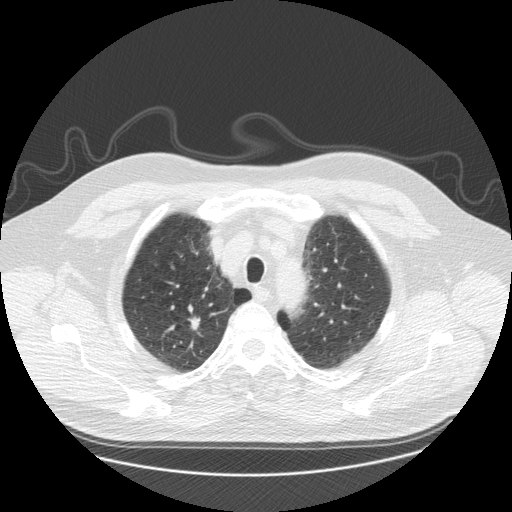
Axial slice from a low-dose chest CT screening exam. Third screening round (two years after baseline). Lung window (W 1500 / L -600 HU). 2.5 mm slice thickness. Slice 30 of 173 in the series. 512 × 512 image matrix, field of view 400 × 400 mm. Male, age 61 years at enrolment. Former smoker at enrolment.
Expert-annotated lung lesion, bounding box [x1, y1, x2, y2] px = [173, 304, 213, 337]. Reader record for this screening exam (exam-level; its link to the box is not recorded): non-calcified nodule or mass ≥4 mm, right upper lobe, 10 × 7 mm, smooth margins, soft tissue attenuation, pre-existing on the prior screen: yes; interval growth: yes.